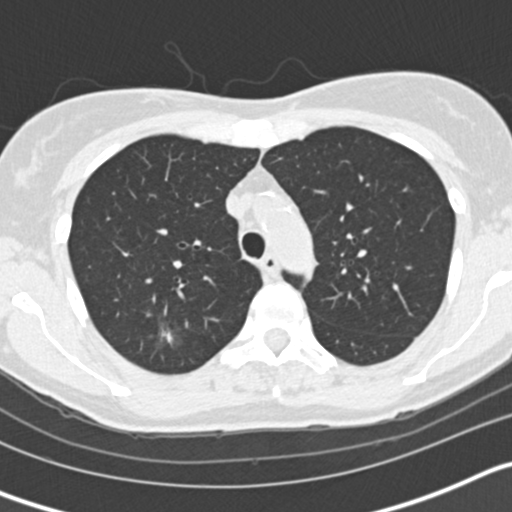
Axial slice from a low-dose chest CT screening exam; second annual screen; lung window (W 1500 / L -600 HU); 2 mm slice thickness; 120 kVp; 512 × 512 image matrix. Female, age 58 years at enrolment. Current smoker at enrolment.
Expert reader's lesion annotation, box from (x=137, y=317) to (x=196, y=366) px. The screening reader recorded 3 non-calcified nodules or masses ≥4 mm on this exam (right upper lobe, left upper lobe, left lower lobe); which of them this box marks is not recorded. Official screen result: positive, other.